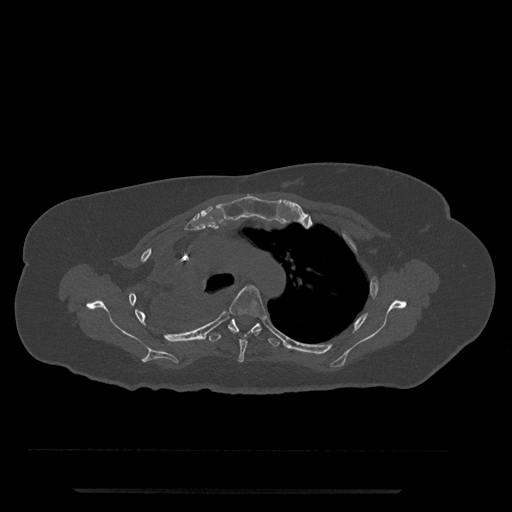
CT including the spine, one axial slice; position 570 of 797 along the scan axis; reconstruction kernel Br40s/3; 120 kVp; bone window (W 1800 / L 400 HU); 512 × 512 image matrix. Patient: female, 51 years. From the clinical record (not read from this slice): primary cancer: neuro.
Annotated regions visible in this slice (semi-automatically segmented with operator editing):
- T4 vertebra: bounding box [x1, y1, x2, y2] px = [229, 285, 267, 363]
- T5 vertebra: [209, 318, 281, 347]